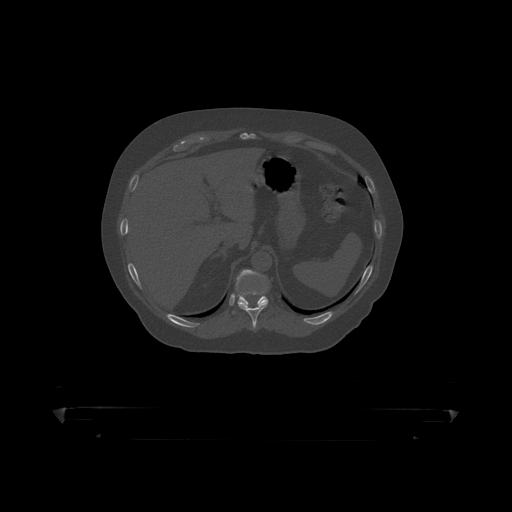
CT including the spine, one axial slice. Position 207 of 390 along the scan axis. Reconstruction kernel STANDARD. 120 kVp. Bone window (W 1800 / L 400 HU). 1.25 mm slice thickness. 512 × 512 image matrix, field of view 650 × 650 mm. Patient: male, 60 years. Case-level facts recorded for this patient, not image findings: primary cancer: prostate.
Annotated regions visible in this slice (semi-automatically segmented with operator editing):
- T10 vertebra: bounding box [x1, y1, x2, y2] px = [239, 277, 269, 319]
- T11 vertebra: [233, 271, 268, 314]